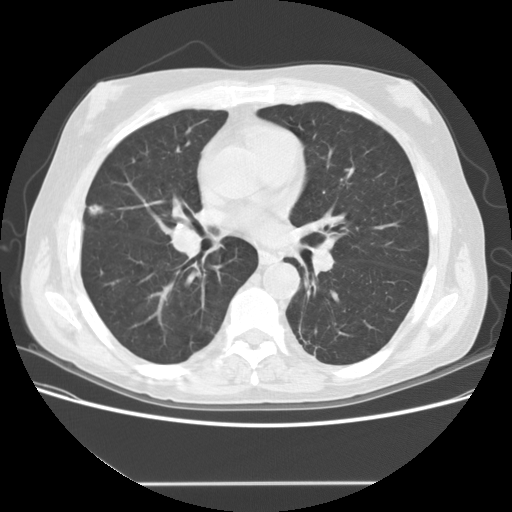
Low-dose screening chest CT, one axial slice; reconstruction kernel STANDARD; lung window (W 1500 / L -600 HU); 2.5 mm slice thickness; 512 × 512 image matrix.
Outlined on this slice (outlined manually by an expert reader):
- lesion 2 (tumor, upper lobe of right lung): bounding box (x1, y1, x2, y2) in pixels: (89, 205, 103, 215)